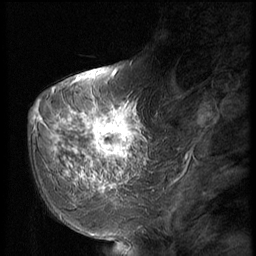
Breast MRI (dynamic contrast-enhanced), one sagittal slice. Slice 19 of 56 in the series (ordered by position). Dynamic contrast-enhanced series, image 2 of 2 at this slice position (ordered by acquisition). 1.5 T. TE 4.2 ms, TR 9 ms. 2.5 mm slice thickness. 256 × 256 image matrix, field of view 180 × 180 mm. Female patient, age 51 years. Case-level facts recorded for this patient, not image findings: setting: breast cancer imaged before/during neoadjuvant chemotherapy; receptor status: triple-negative.
Annotated regions visible in this slice (semi-automatic segmentation, software-assisted and operator-edited):
- analysis volume of interest (the breast-tissue region the enhancement analysis was run in; not a lesion): bounding box [x1, y1, x2, y2] px = [60, 98, 147, 197]
- tumour enhancement mask (voxels above the 140 % enhancement threshold inside the analysis volume of interest): [68, 104, 135, 193]